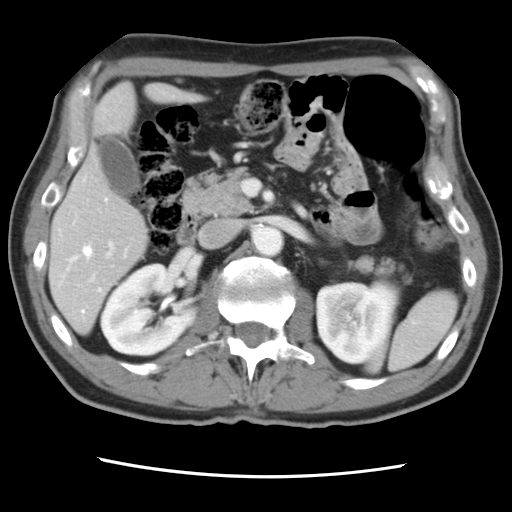
Contrast-enhanced abdominal CT, one axial slice; slice 39 of 83 in the series (ordered by position); 120 kVp; intravenous contrast given; soft-tissue window (W 400 / L 40 HU); 5 mm slice thickness; 512 × 512 image matrix, field of view 321 × 321 mm. Male patient, age 69 years. Case-level facts recorded for this patient, not image findings: diagnosis: colorectal cancer liver metastases, imaged before liver resection; multiple liver metastases: yes; largest metastasis: 3.5 cm; disease in both lobes: no.
Annotated regions visible in this slice (expert manual segmentation):
- hepatic veins: bounding box [x1, y1, x2, y2] px = [71, 198, 108, 312]
- liver: [51, 86, 192, 331]
- planned liver remnant (the part of the liver to remain after resection): [51, 153, 149, 331]
- portal vein (with intrahepatic branches): [73, 176, 115, 283]